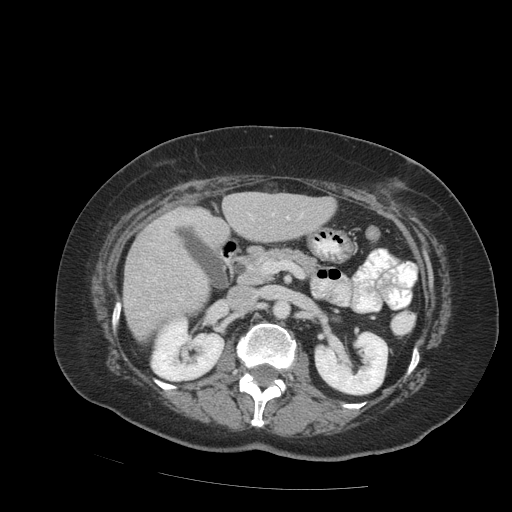
Contrast-enhanced abdominal CT (liver protocol), one axial slice; position 37 of 99 along the scan axis; reconstruction kernel STANDARD; soft-tissue window (W 400 / L 40 HU); 2.5 mm slice thickness; 512 × 512 image matrix, field of view 400 × 400 mm. Case-level facts recorded for this patient, not image findings: diagnosis: hepatocellular carcinoma (patient treated with transarterial chemoembolisation; whether this scan precedes or follows treatment is not stated here); TNM stage (as recorded): Stage-IVB; Child-Pugh class: A; tumour differentiation: moderately differentiated; tumour nodularity: uninodular.
Structures marked on this image (semi-automatically segmented with operator editing):
- liver parenchyma outside the tumour (the mass and vessels are separate outlines, so this box may not span the whole liver): bounding box (x1, y1, x2, y2) in pixels: (124, 192, 334, 340)
- liver vessels: (249, 214, 302, 220)